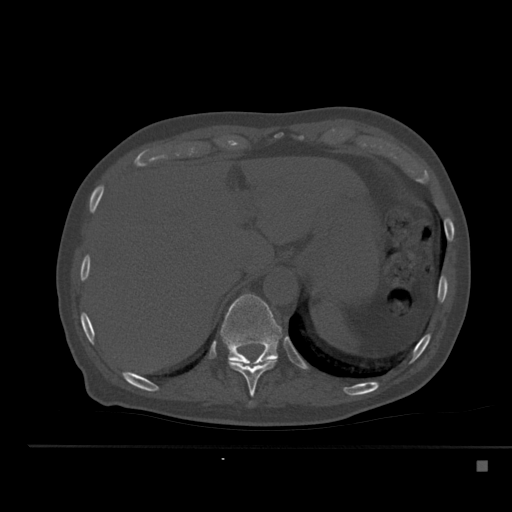
CT including the spine, one axial slice. Slice 259 of 517 in the series (ordered by position). 120 kVp. Bone window (W 1800 / L 400 HU). 1.5 mm slice thickness. 512 × 512 image matrix, field of view 408 × 408 mm. Patient: male, 70 years. Case-level facts recorded for this patient, not image findings: primary cancer: renal.
Outlined on this slice (semi-automatic segmentation, software-assisted and operator-edited):
- T10 vertebra: box from (x=228, y=358) to (x=278, y=396) px
- T11 vertebra: (x=220, y=294)–(x=282, y=363)